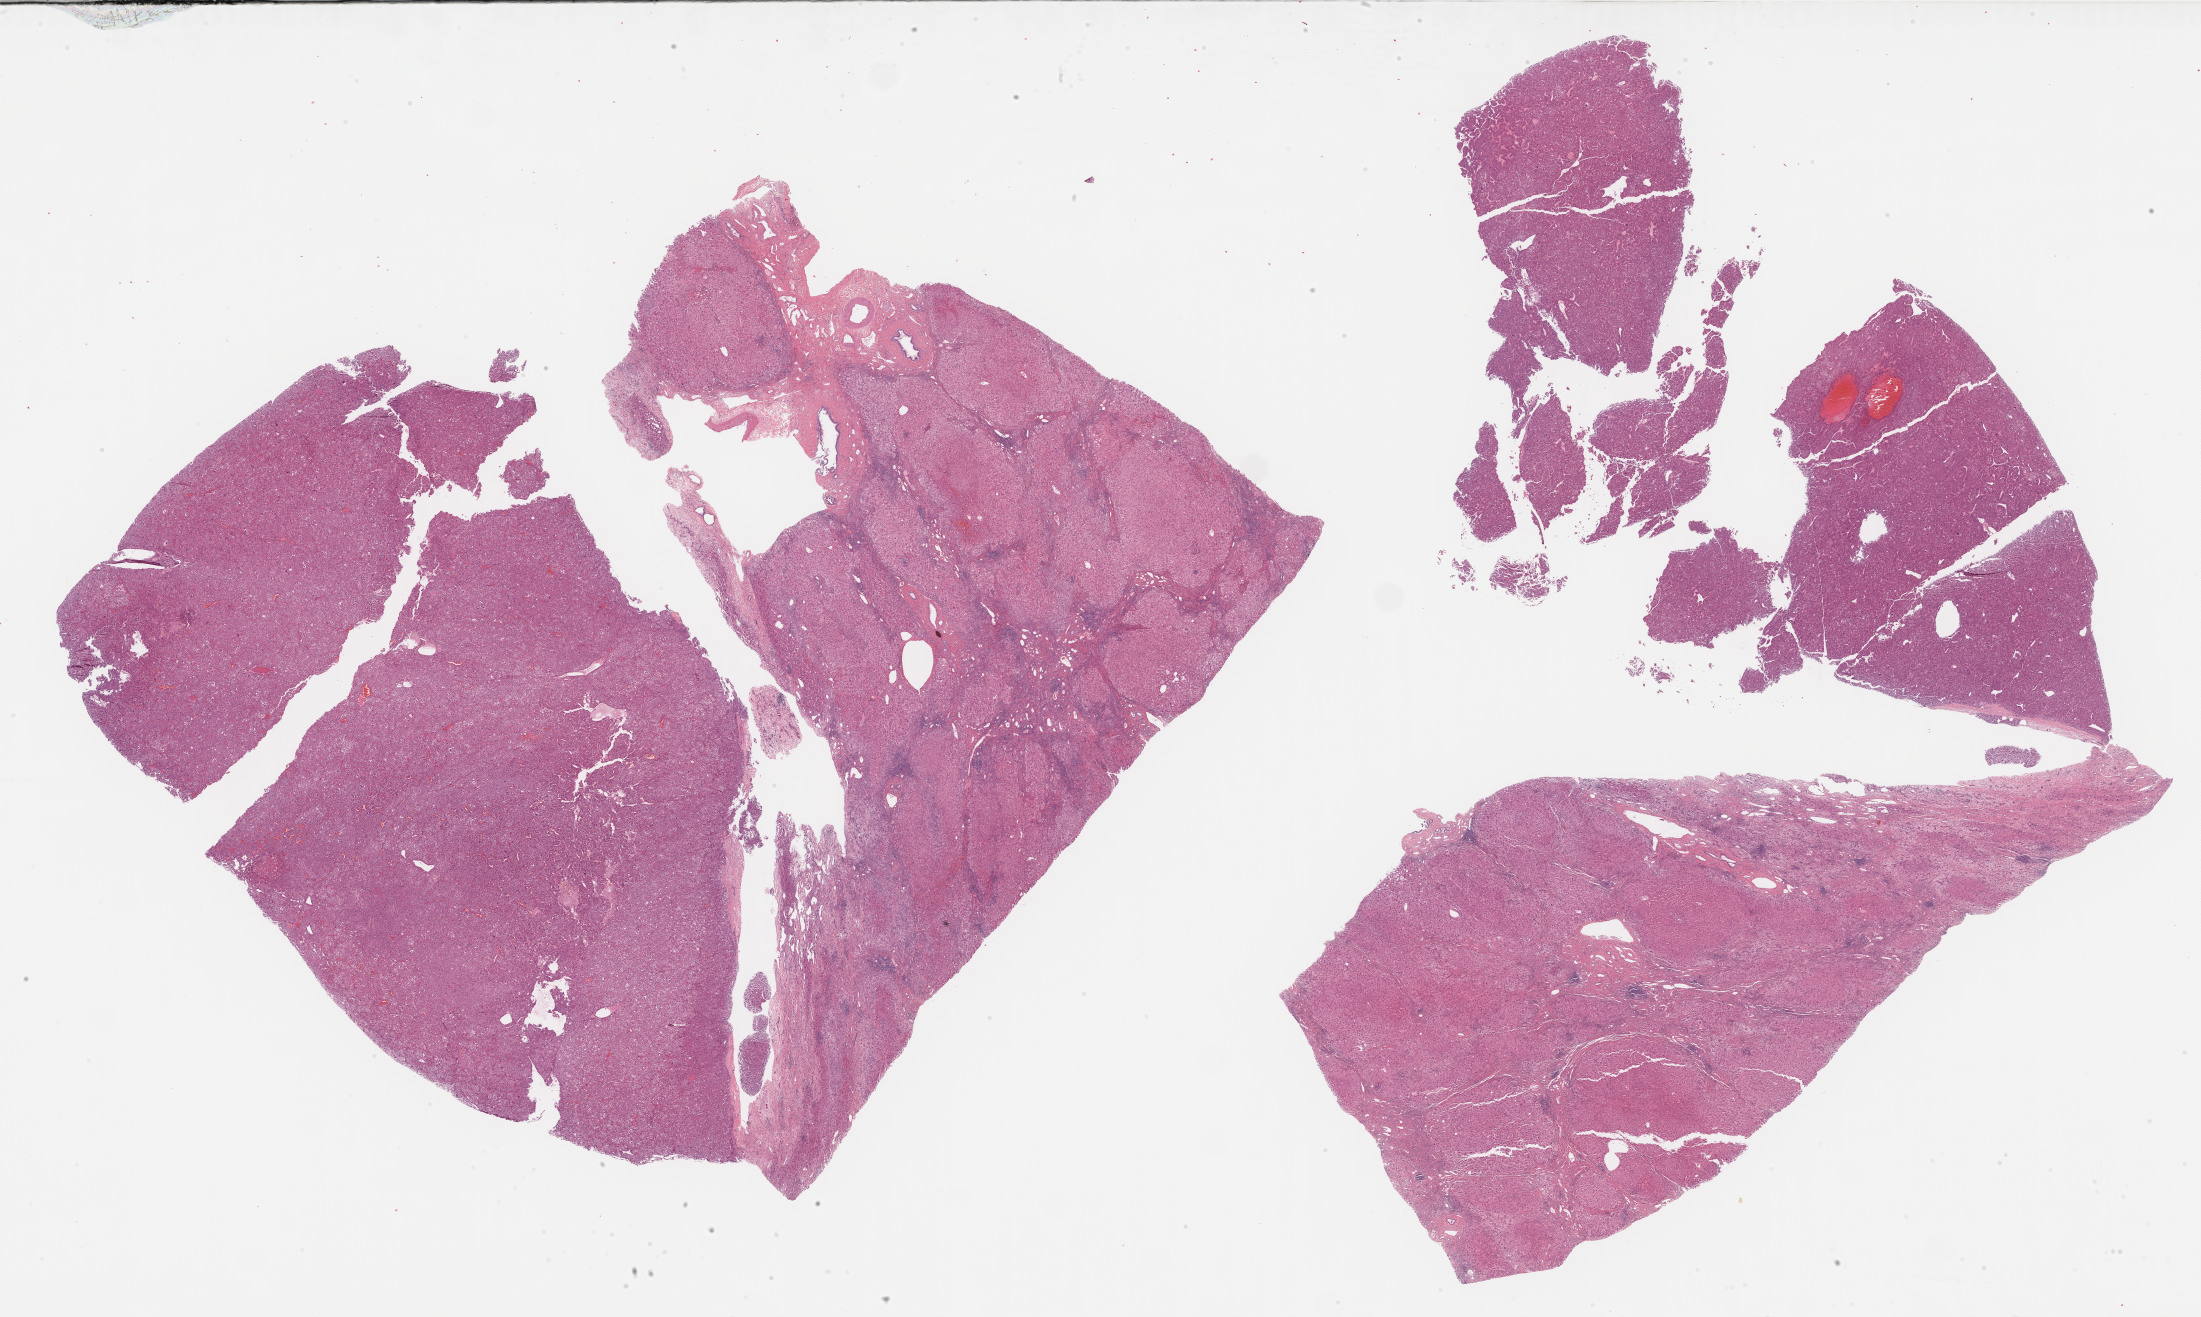
Whole-slide histology image, H&E, a low-resolution overview of the entire scanned area, about 35.6 x 21.3 mm, formalin-fixed paraffin-embedded (FFPE) diagnostic section, primary tumour sample from the liver. Female, age 72 years at initial diagnosis. Histologic grade: G2 (moderately differentiated).
AJCC pathologic stage: I (7th edition). Diagnosis: Hepatocellular carcinoma, NOS.